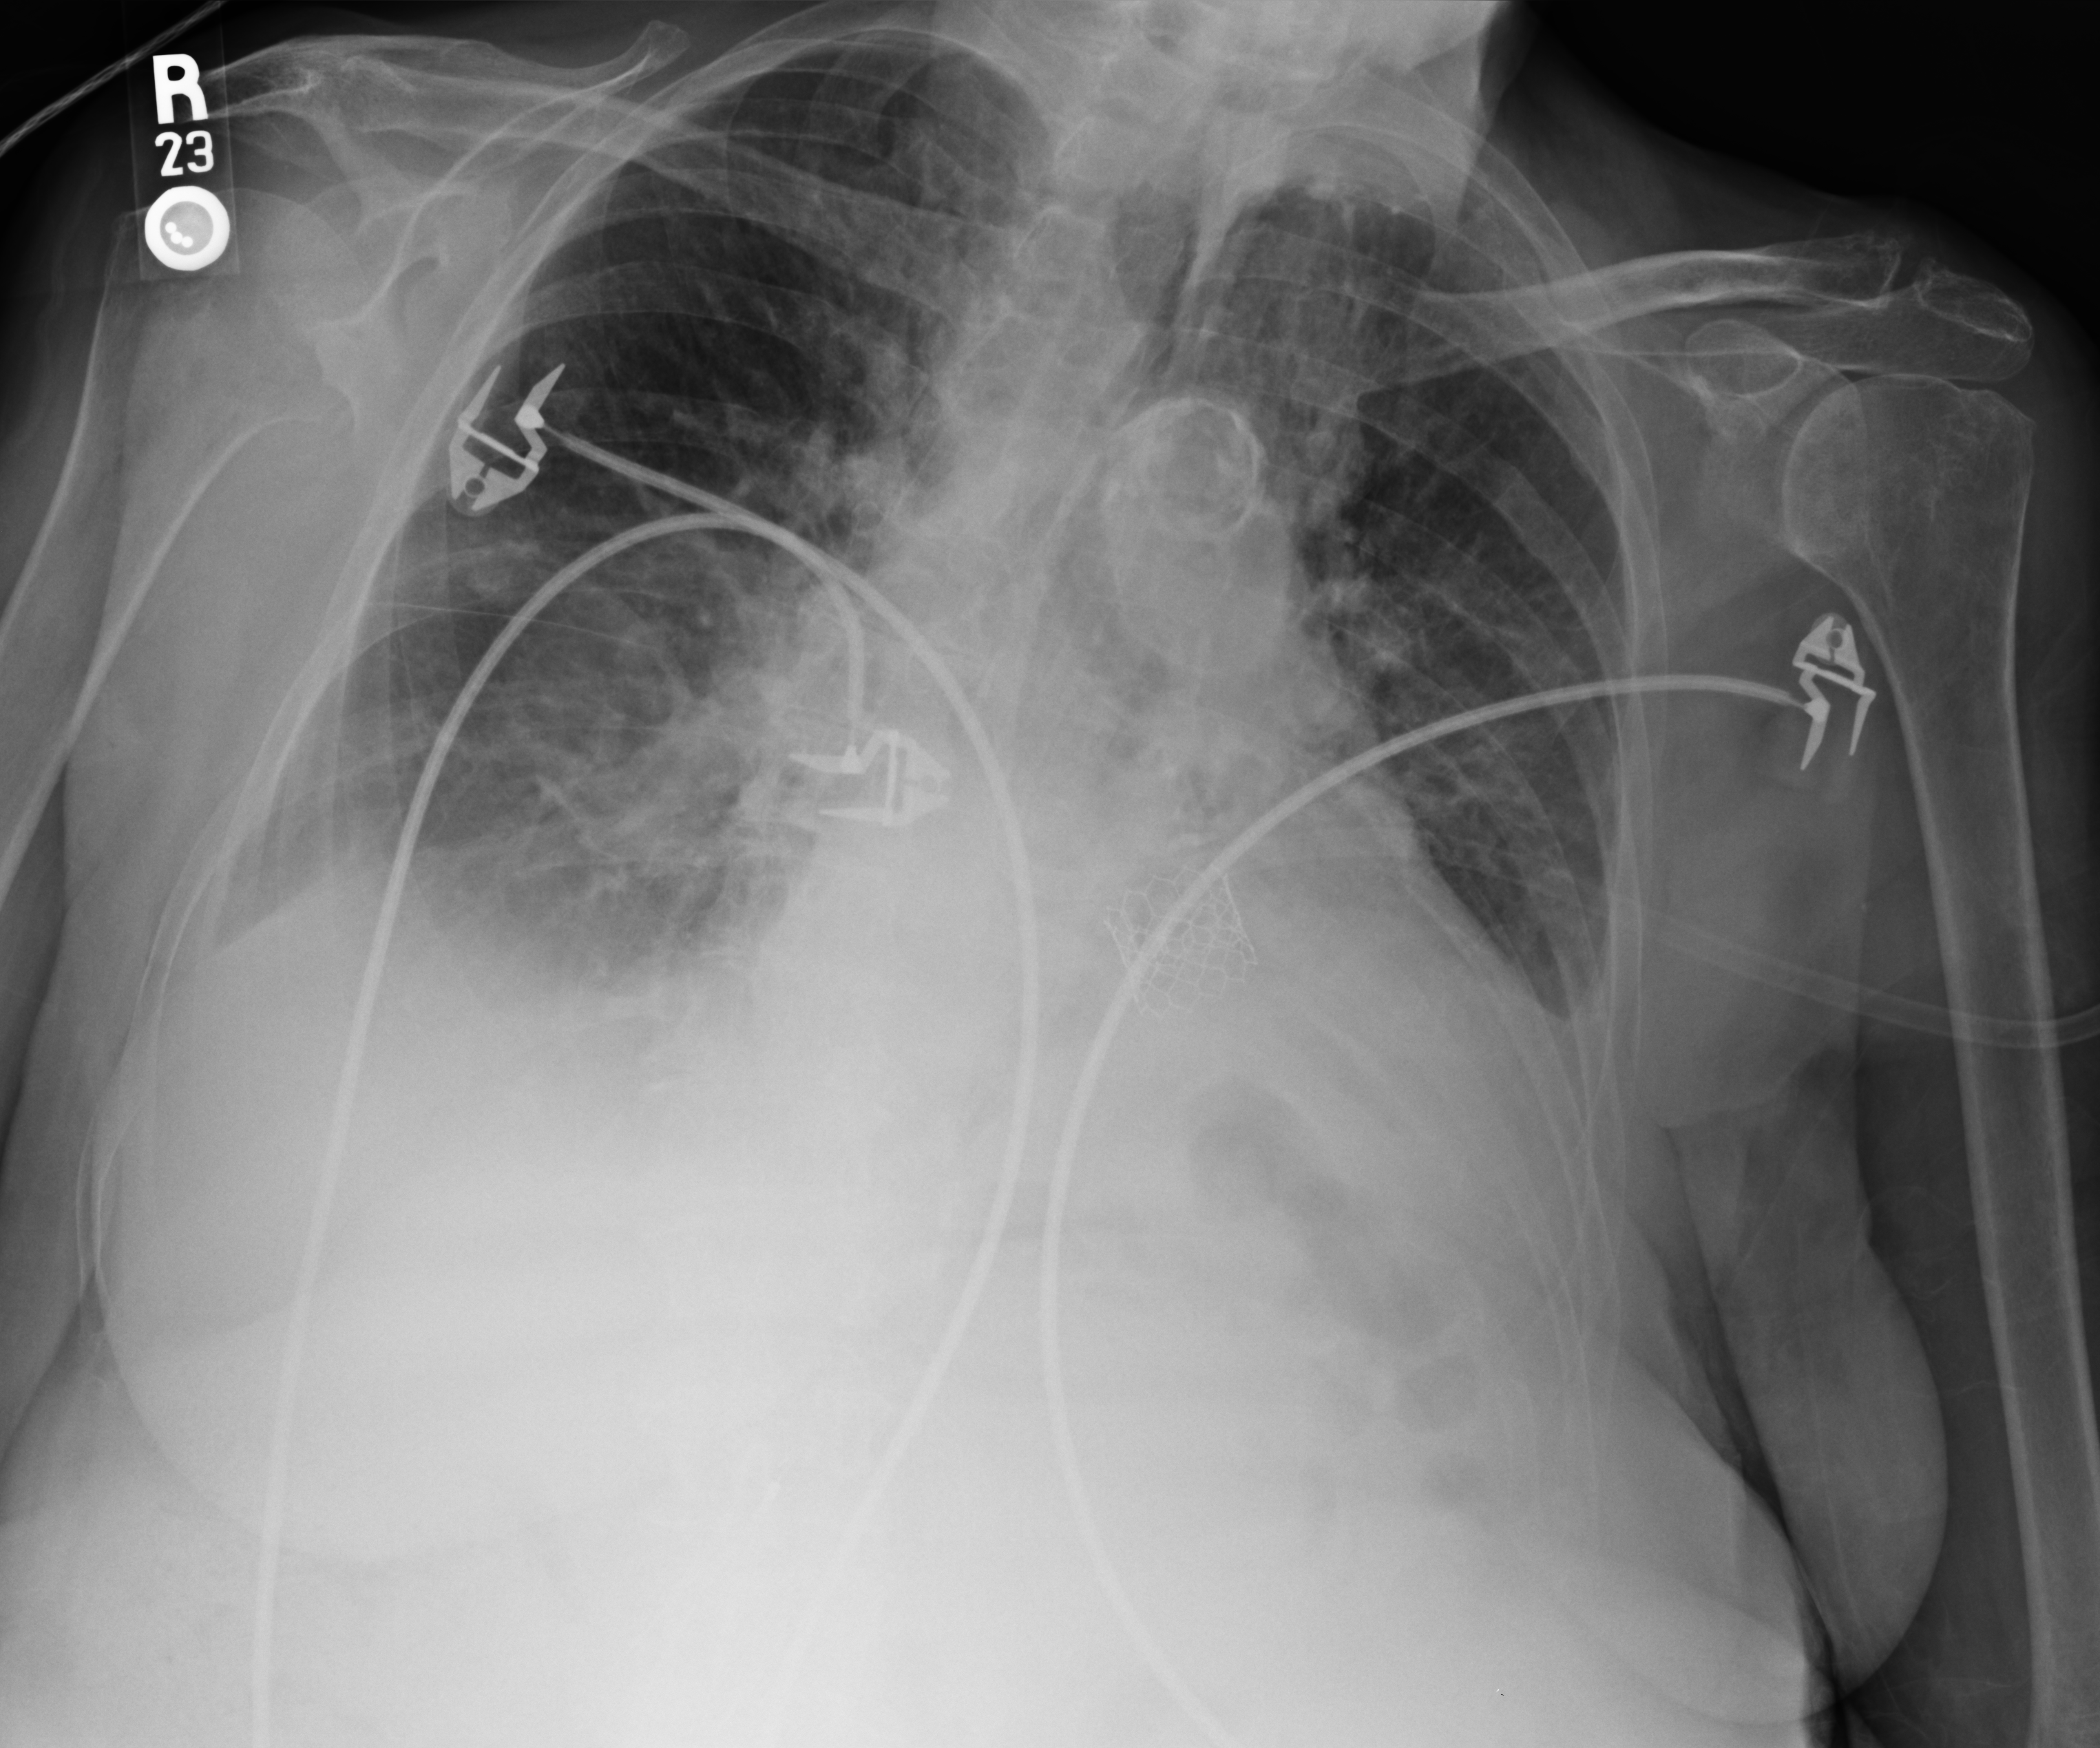
Portable chest radiograph; anteroposterior (AP) projection. Patient hospitalised with COVID-19; female, aged 75–90 years.
Admission-level facts for this patient (not findings on this image; timing relative to this image not recorded): admitted to intensive care during this hospital stay: no; mechanically ventilated during this hospital stay: no.